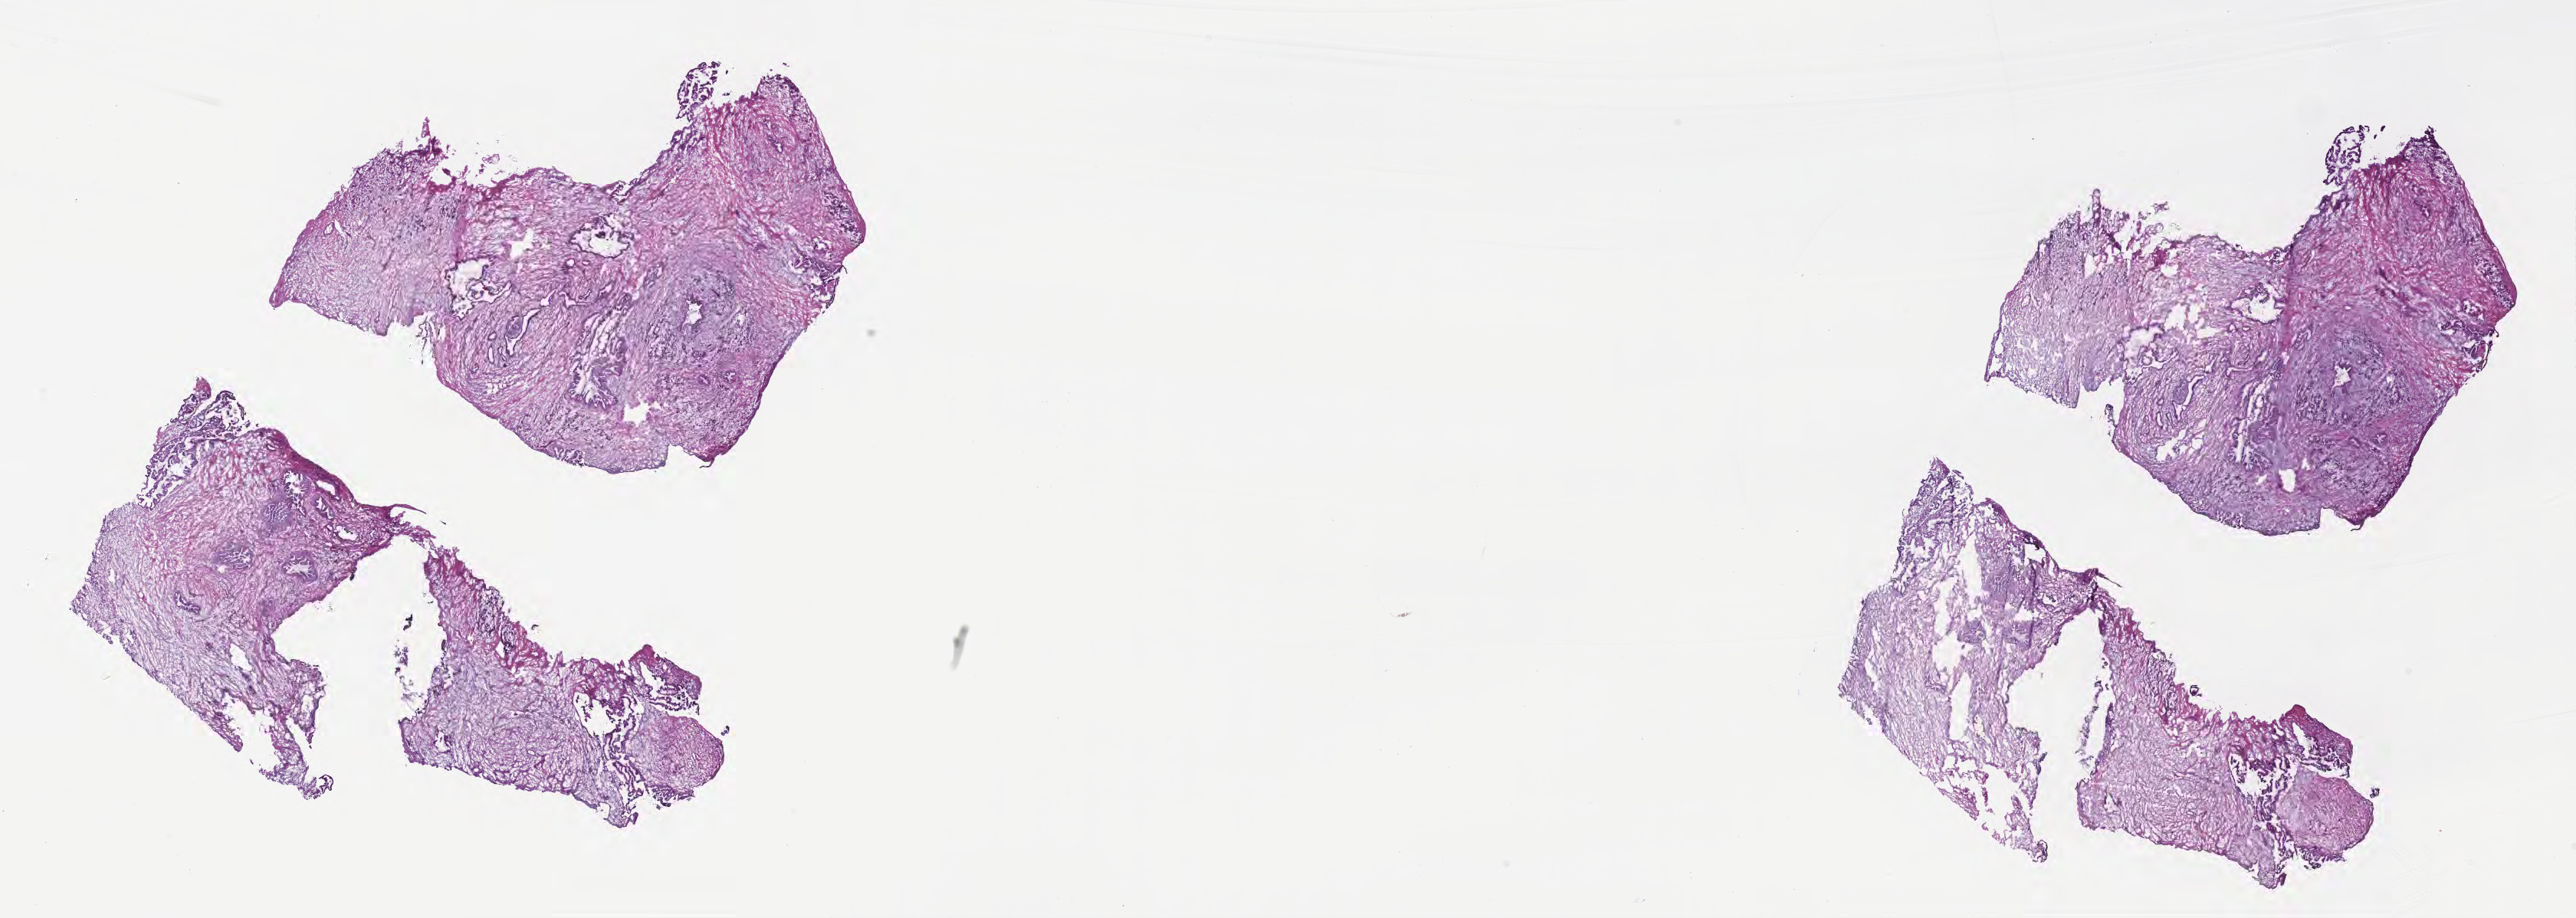
Whole-slide image, haematoxylin and eosin stain, a low-resolution overview of the entire scanned area, about 27.2 x 9.7 mm; frozen section; primary tumor; site: head of pancreas. Male patient; age at initial diagnosis 67 years. Pathologist review of this section (percent, as recorded): tumor cells 100%, tumor nuclei 20%, stromal cells 0%, necrosis 0%, normal cells 0%. Inflammatory infiltration, as recorded: lymphocyte infiltration 0%, monocyte infiltration 0%, neutrophil infiltration 0%.
• histologic diagnosis: Infiltrating duct carcinoma, NOS